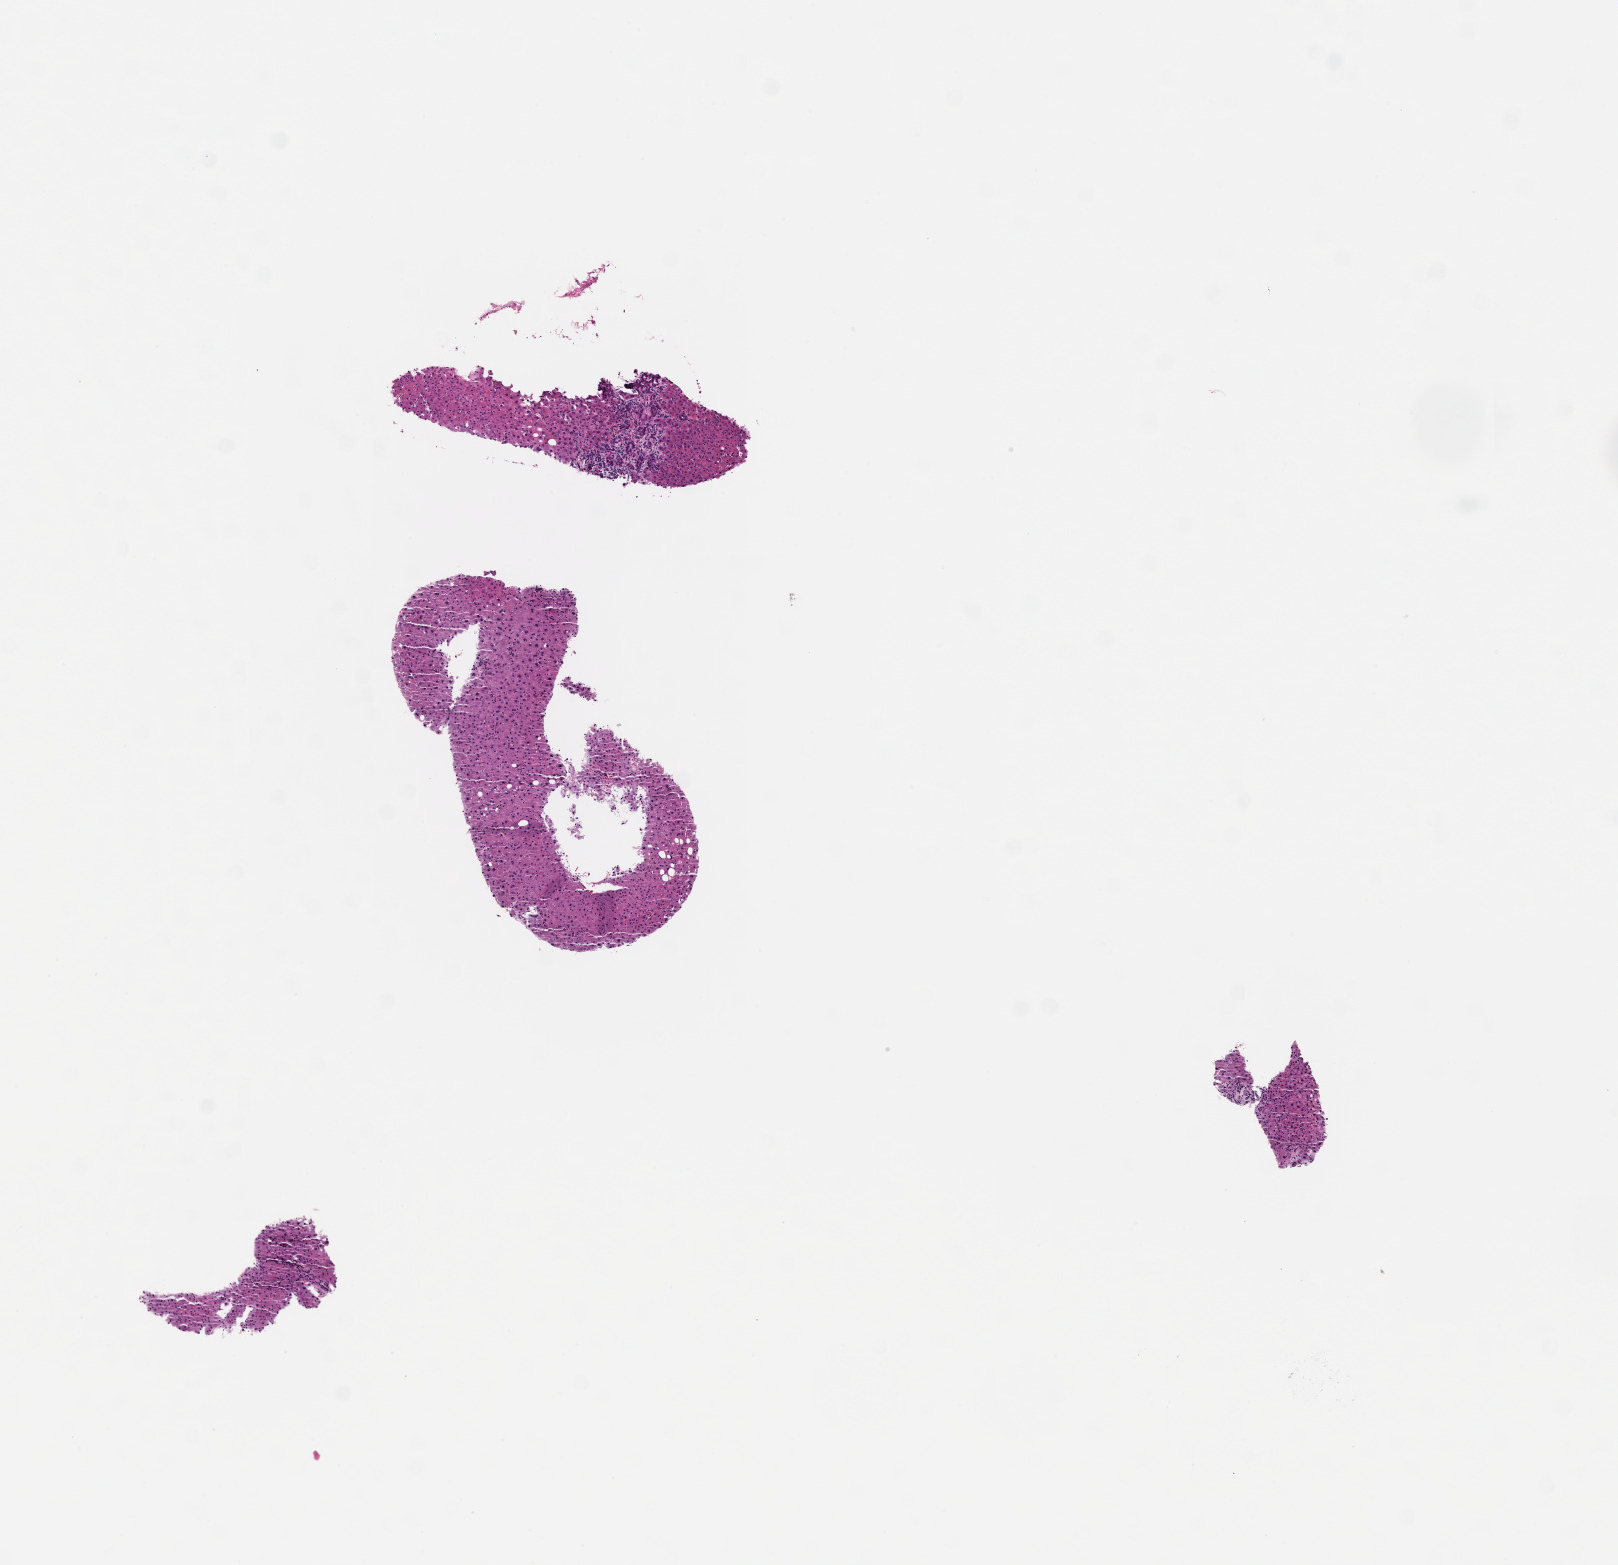
H&E whole-slide image — low-resolution overview of the scanned area, about 6.5 x 6.3 mm. FFPE section. Specimen time point: collected at baseline (before treatment). Patient: female.
This section: metastatic tumor tissue. Primary diagnosis of the patient: Invasive Breast Carcinoma.